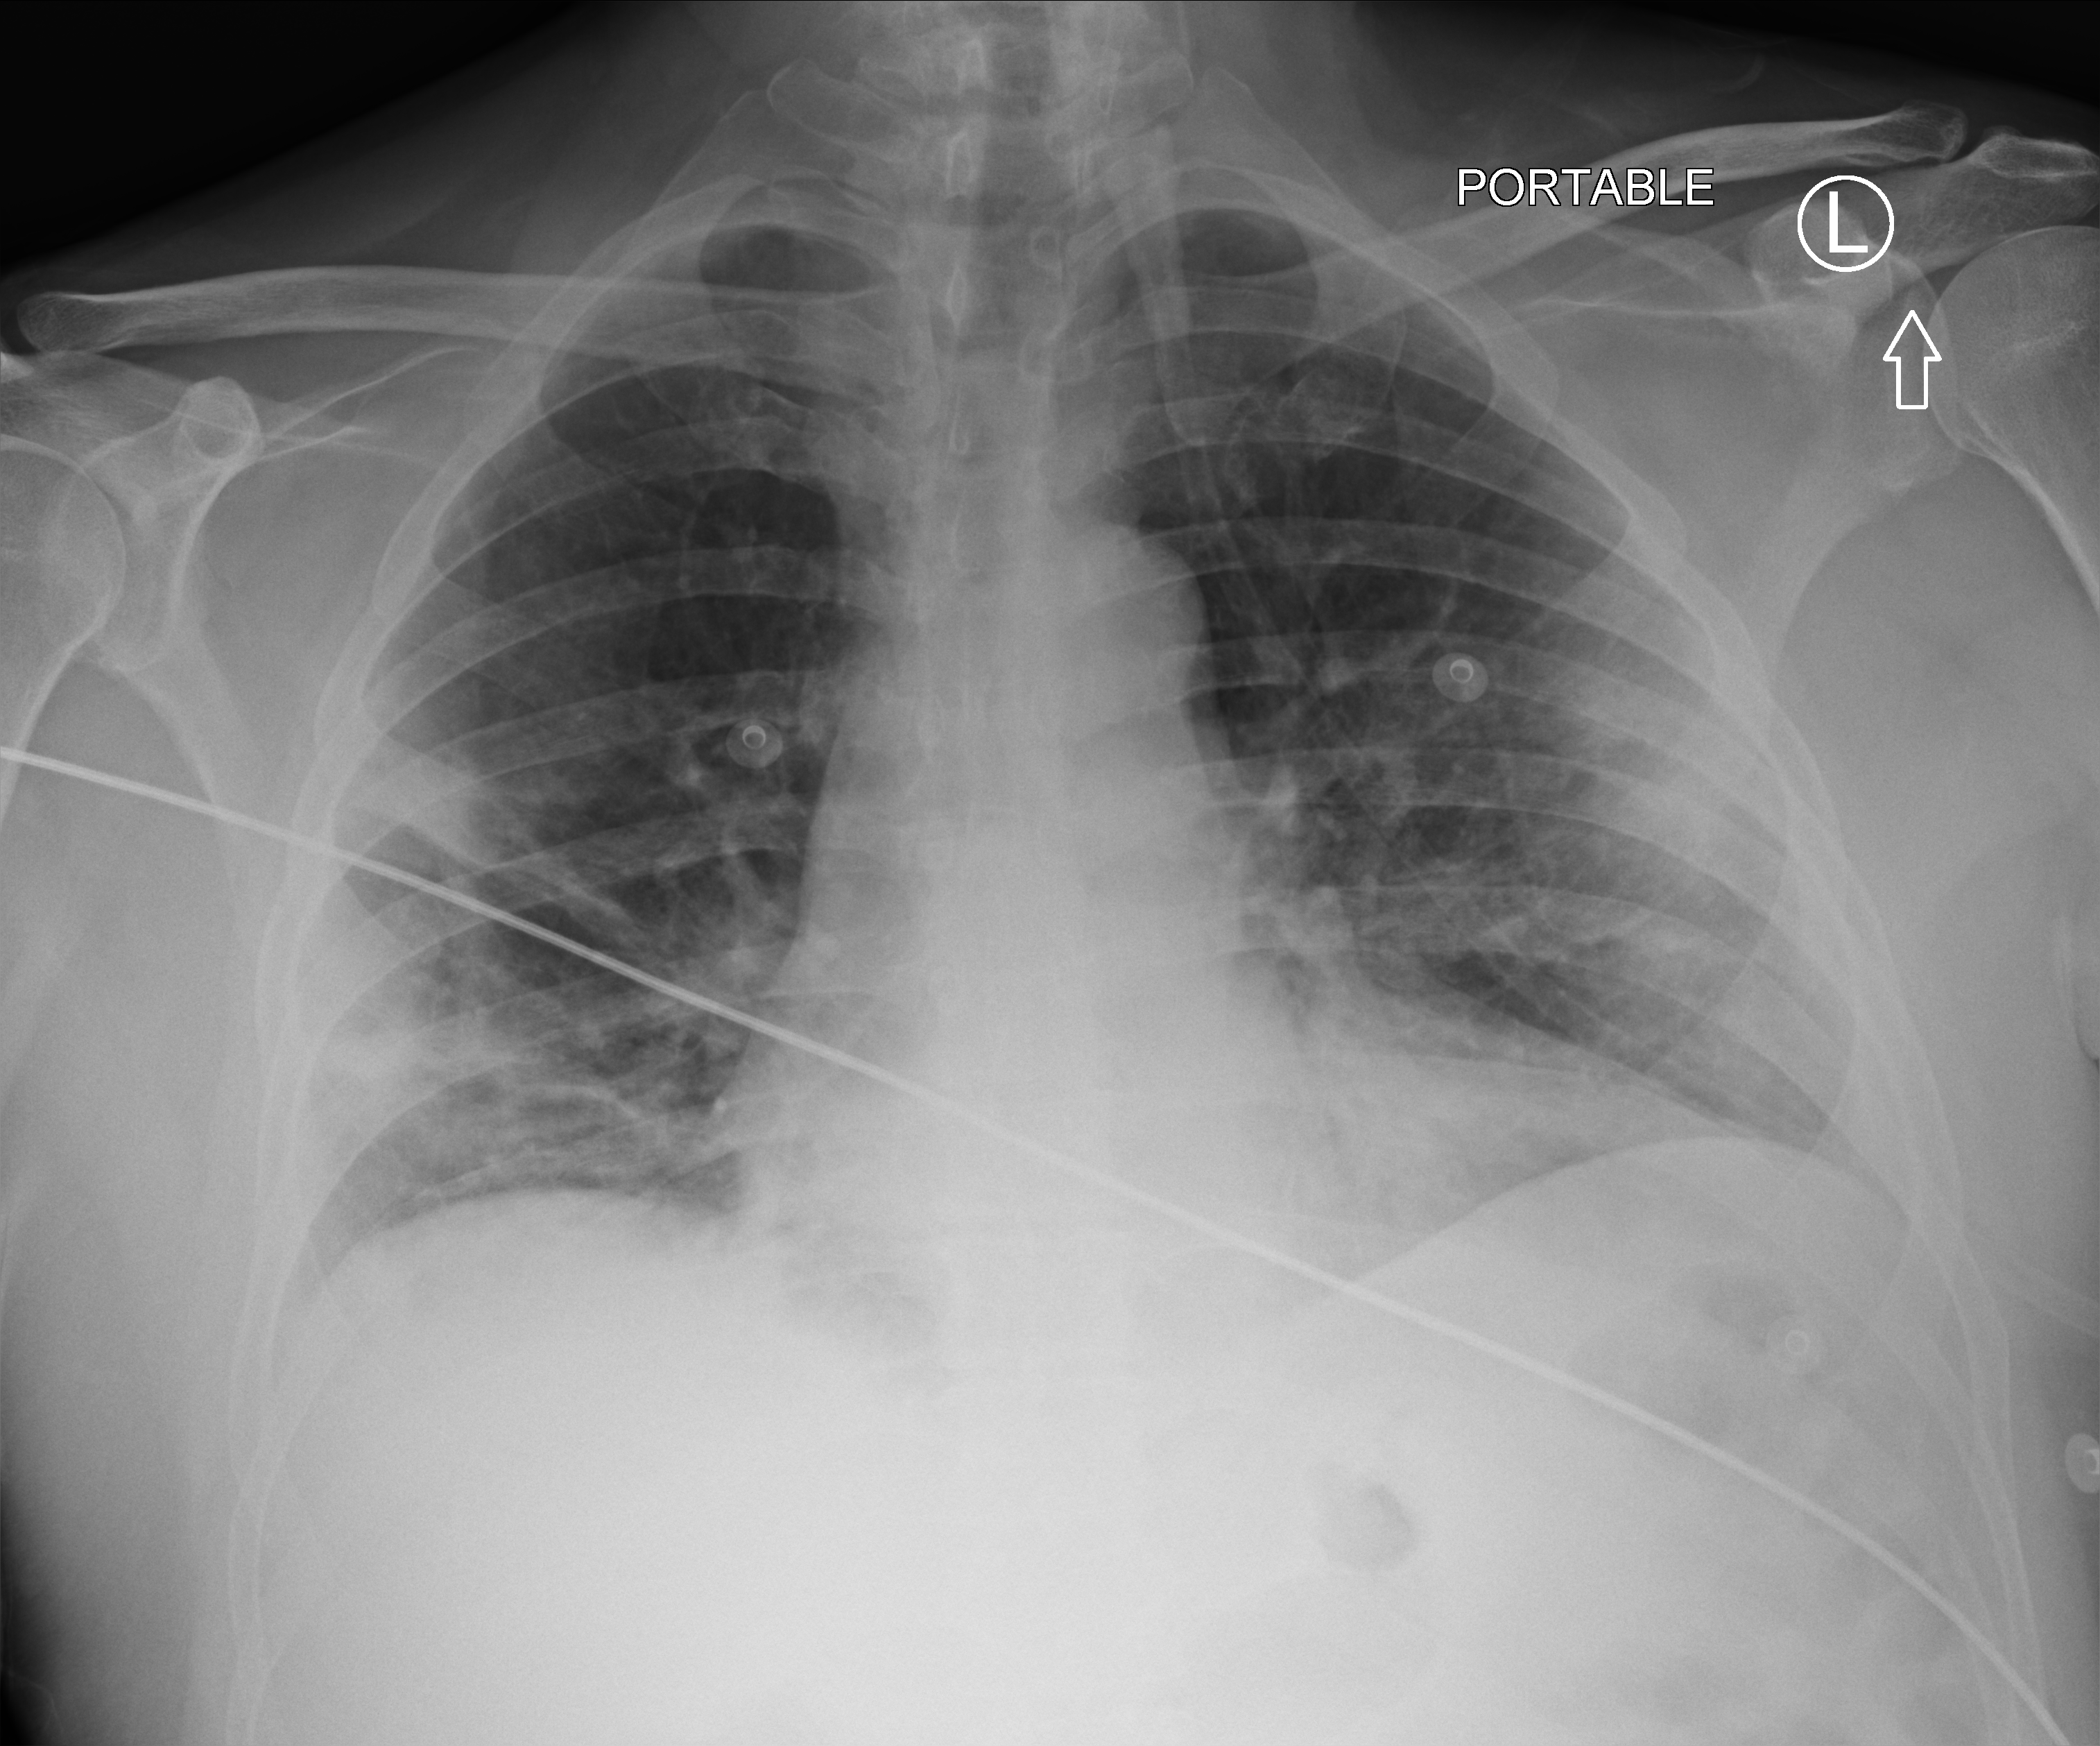
Chest X-ray (portable). Male patient hospitalised with COVID-19, age 60–74 years.
Admission-level facts for this patient (not findings on this image; timing relative to this image not recorded): diabetes (admission record): no; mechanically ventilated during this hospital stay: no; admitted to intensive care during this hospital stay: no.